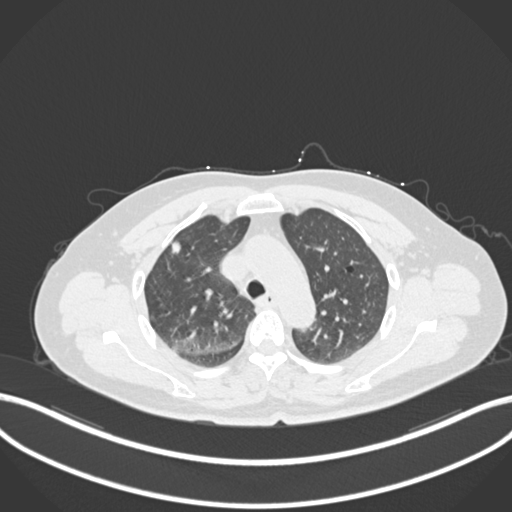
Chest CT, one axial slice. Slice 169 of 223 in the series (ordered by position). Reconstruction kernel B30f. Lung window (W 1500 / L -600 HU). 1 mm slice thickness. 512 × 512 image matrix. Female patient, age 56 years. From the clinical record (not read from this slice): clinical TNM (as recorded): T1c N0 M0.
Outlined on this slice (rectangle marked by the reading radiologist):
- lung tumour (recorded histology: adenocarcinoma): bounding box [x1, y1, x2, y2] px = [169, 235, 190, 258]